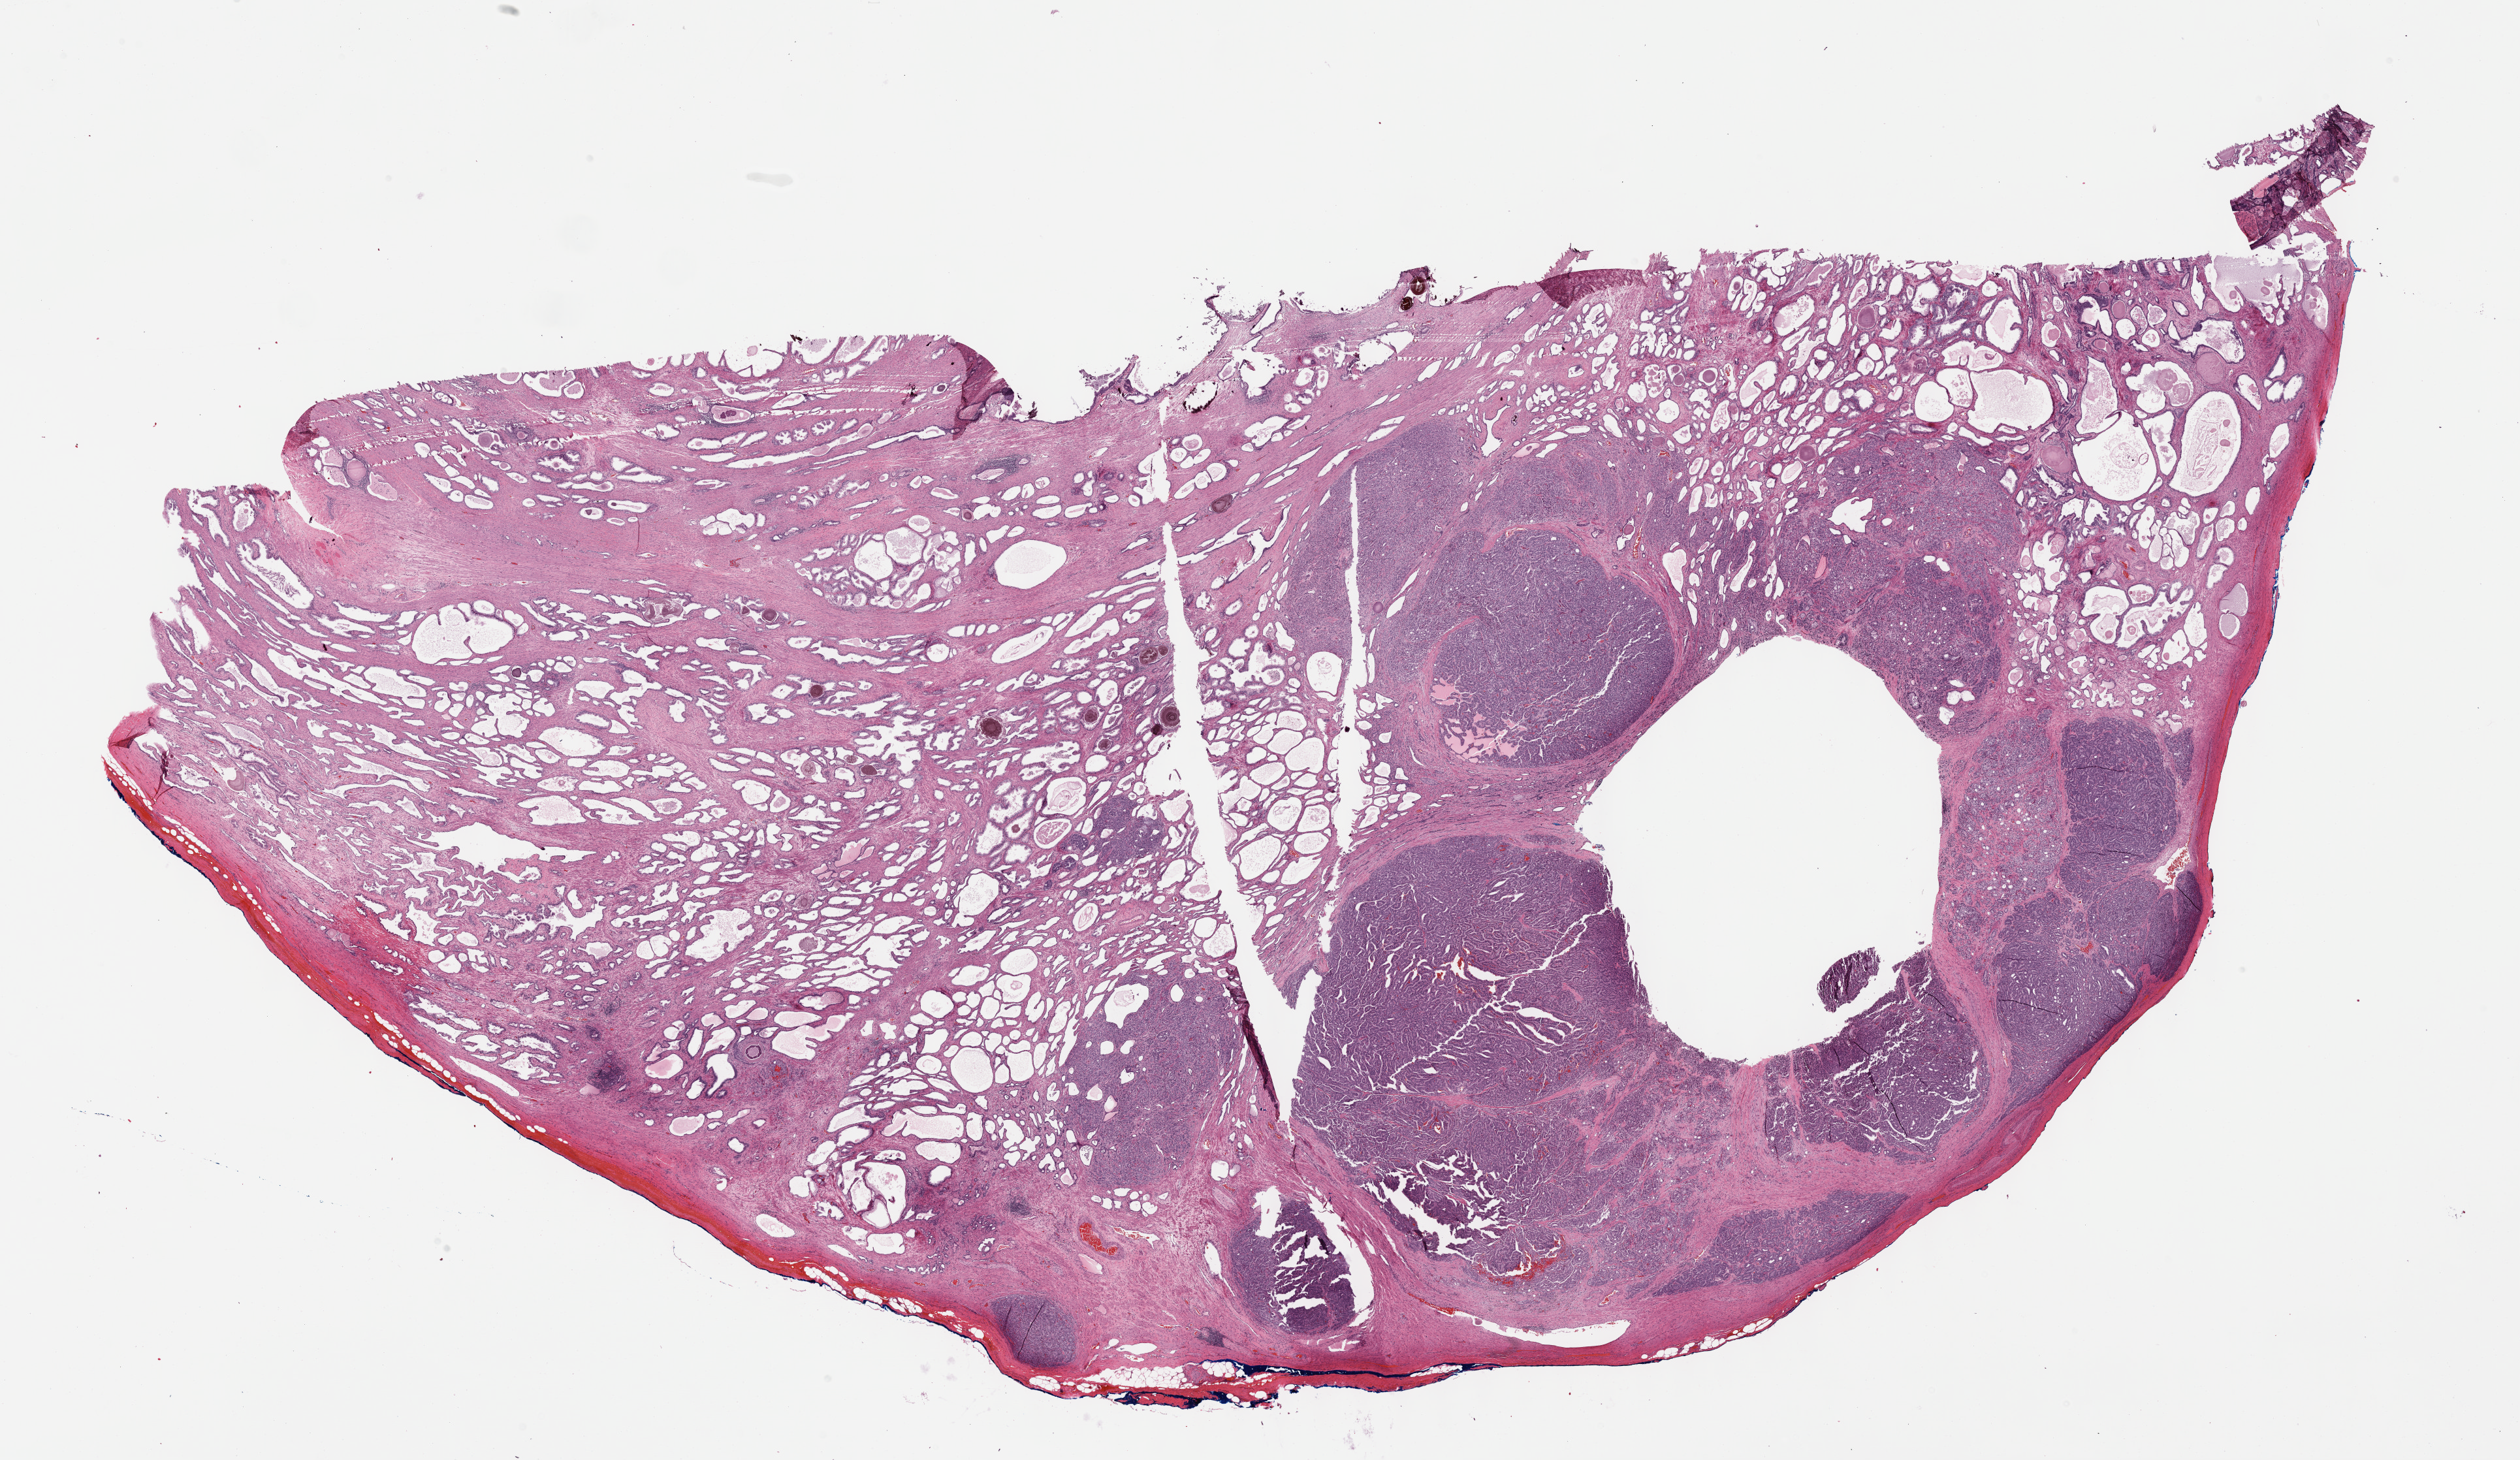
Digitized Hematoxylin and eosin (H&E) stained tissue section (whole slide), a low-resolution overview of the entire scanned area, about 31.2 x 18.1 mm, formalin-fixed paraffin-embedded (FFPE) diagnostic section, sample: primary tumour, prostate. Male, age 69 years at initial diagnosis. Gleason score: 9 (4+5).
Laterality: left. Pathologic diagnosis: Adenocarcinoma, NOS (prostate gland).